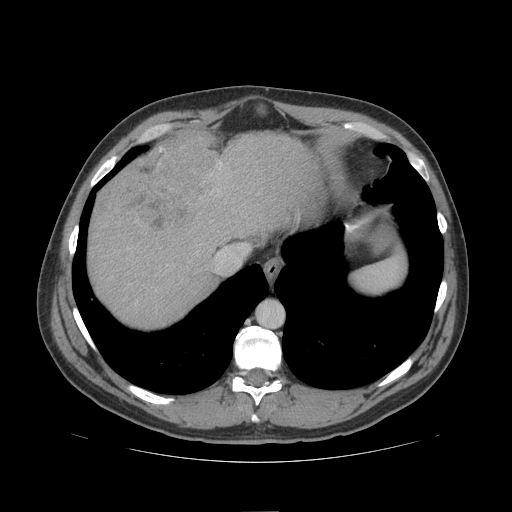
Contrast-enhanced abdominal CT (liver protocol), one axial slice; slice 87 of 109 in the series (ordered by position); reconstruction kernel STANDARD; 140 kVp; soft-tissue window (W 400 / L 40 HU); 2.5 mm slice thickness; 512 × 512 image matrix, field of view 420 × 420 mm. From the clinical record (not read from this slice): diagnosis: hepatocellular carcinoma (patient treated with transarterial chemoembolisation; whether this scan precedes or follows treatment is not stated here); TNM stage (as recorded): Stage-IIIB; Child-Pugh class: A; tumour differentiation: poorly differentiated; tumour nodularity: multinodular.
Annotated regions visible in this slice (semi-automatic segmentation, software-assisted and operator-edited):
- liver parenchyma outside the tumour (the mass and vessels are separate outlines, so this box may not span the whole liver): bounding box <88,132,318,326> (left, top, right, bottom; pixels)
- mass: <105,139,212,237>